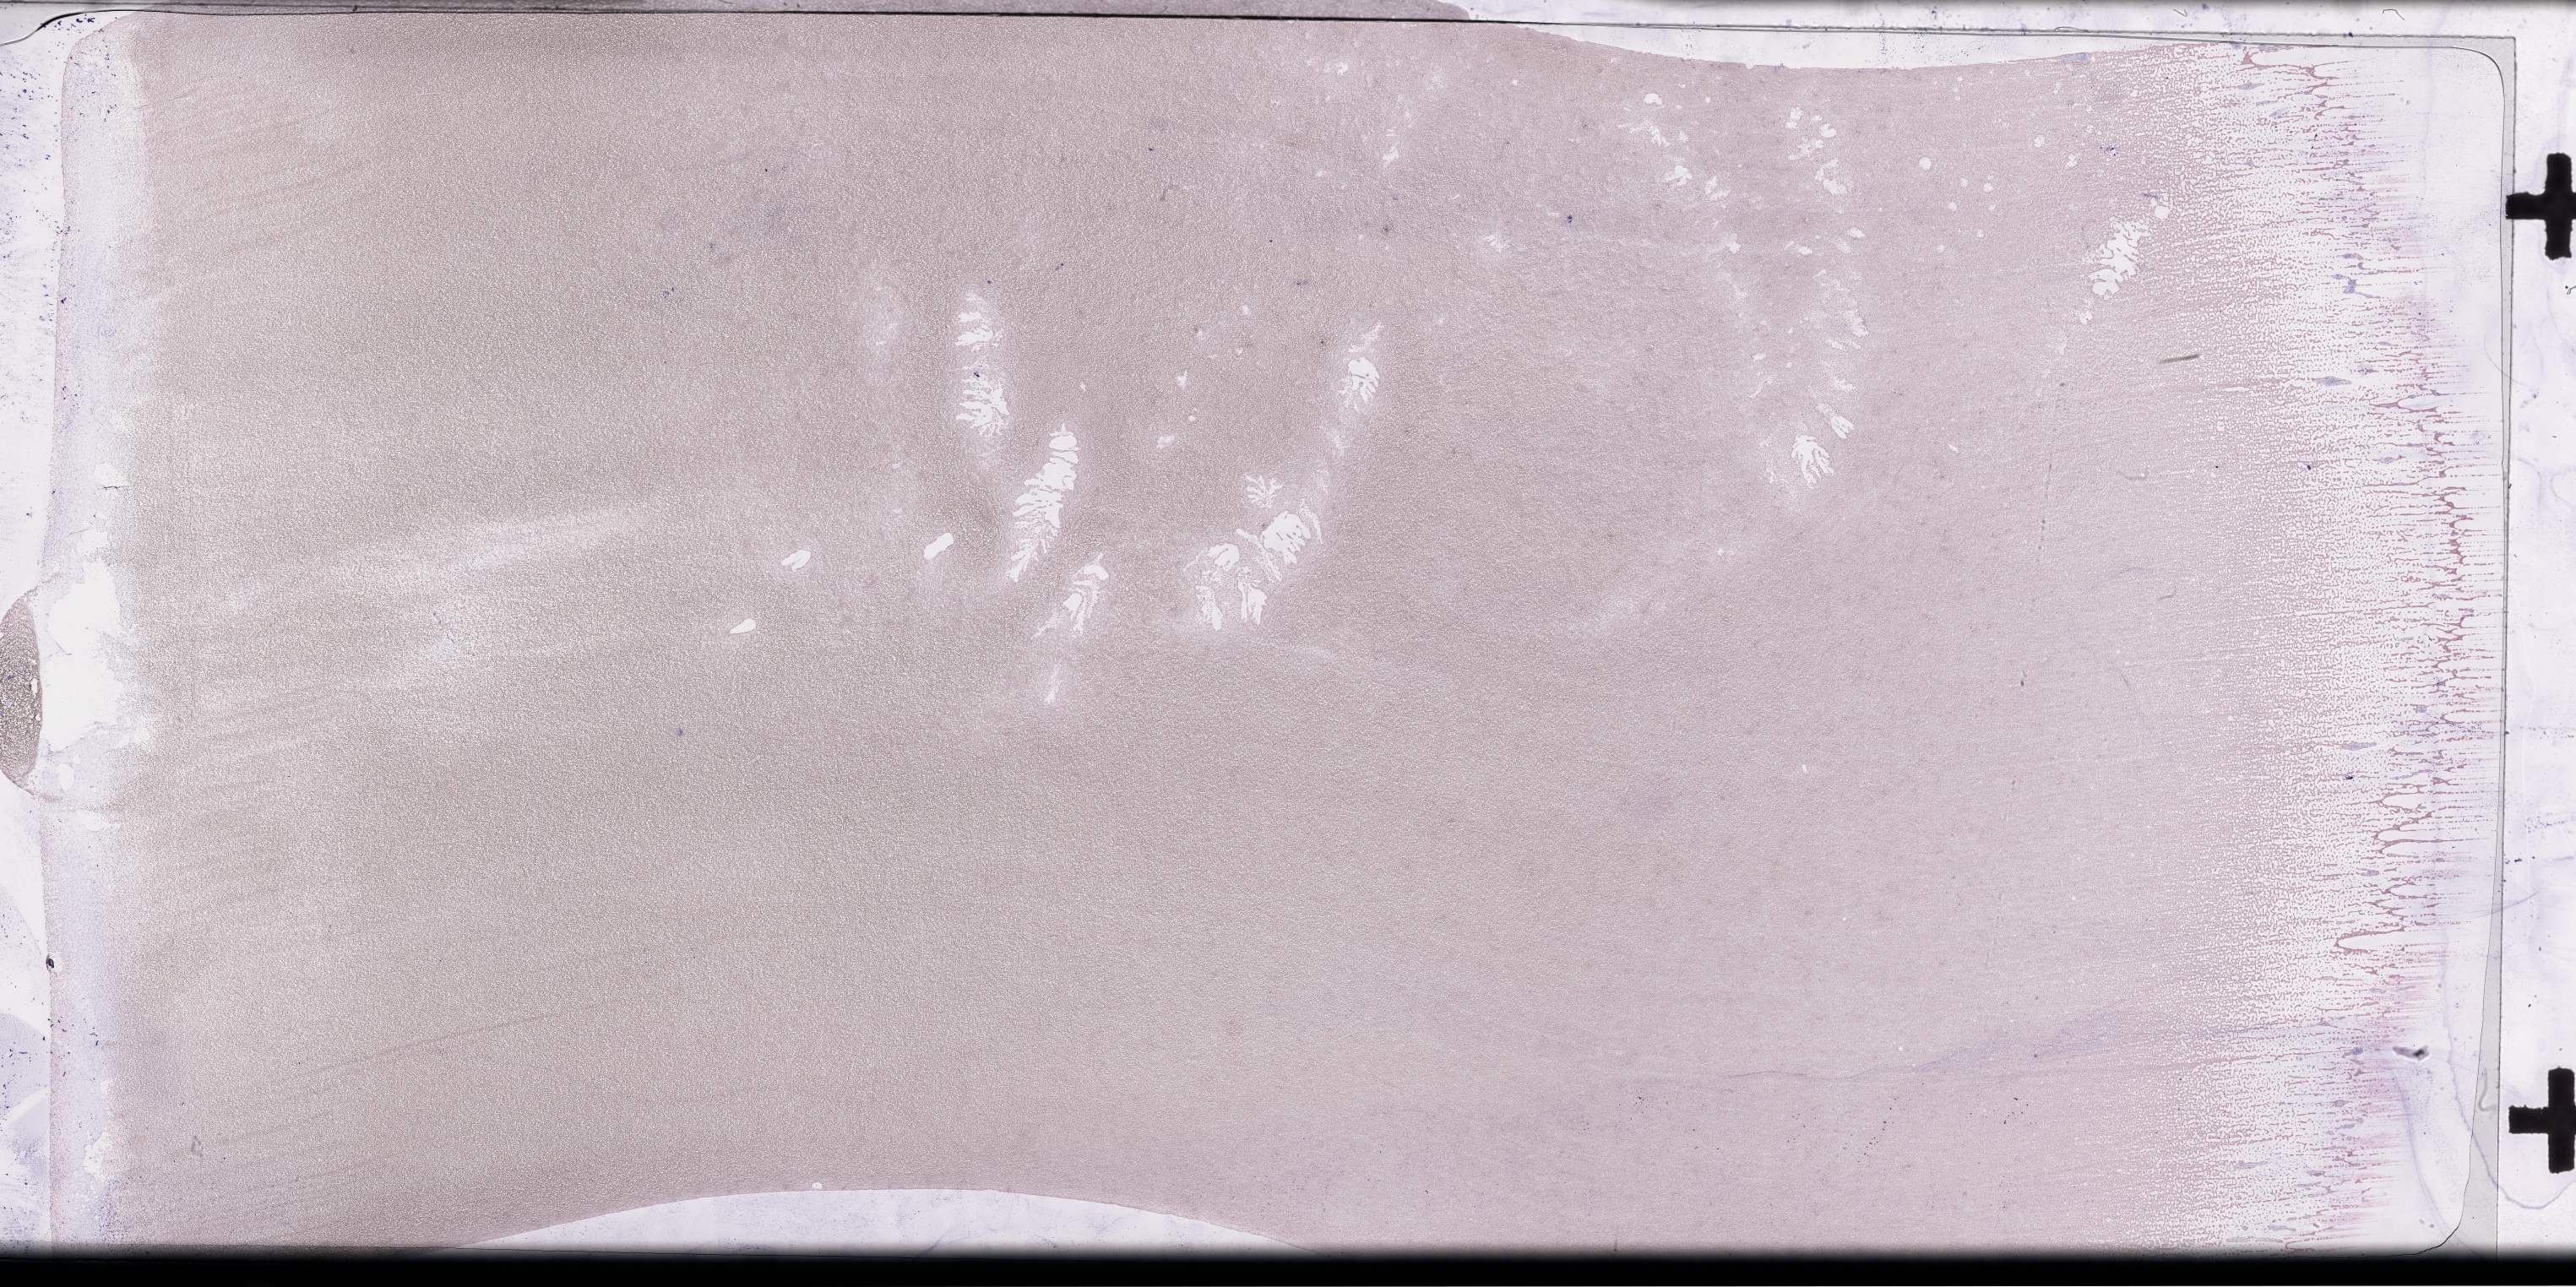
Whole-slide image of a whole blood smear, Wright-Giemsa stain, a low-resolution overview of the entire scanned area, about 49.3 x 24.6 mm; EDTA-anticoagulated smear. Patient sex: male.
• patient diagnosis: Plasma Cell Myeloma